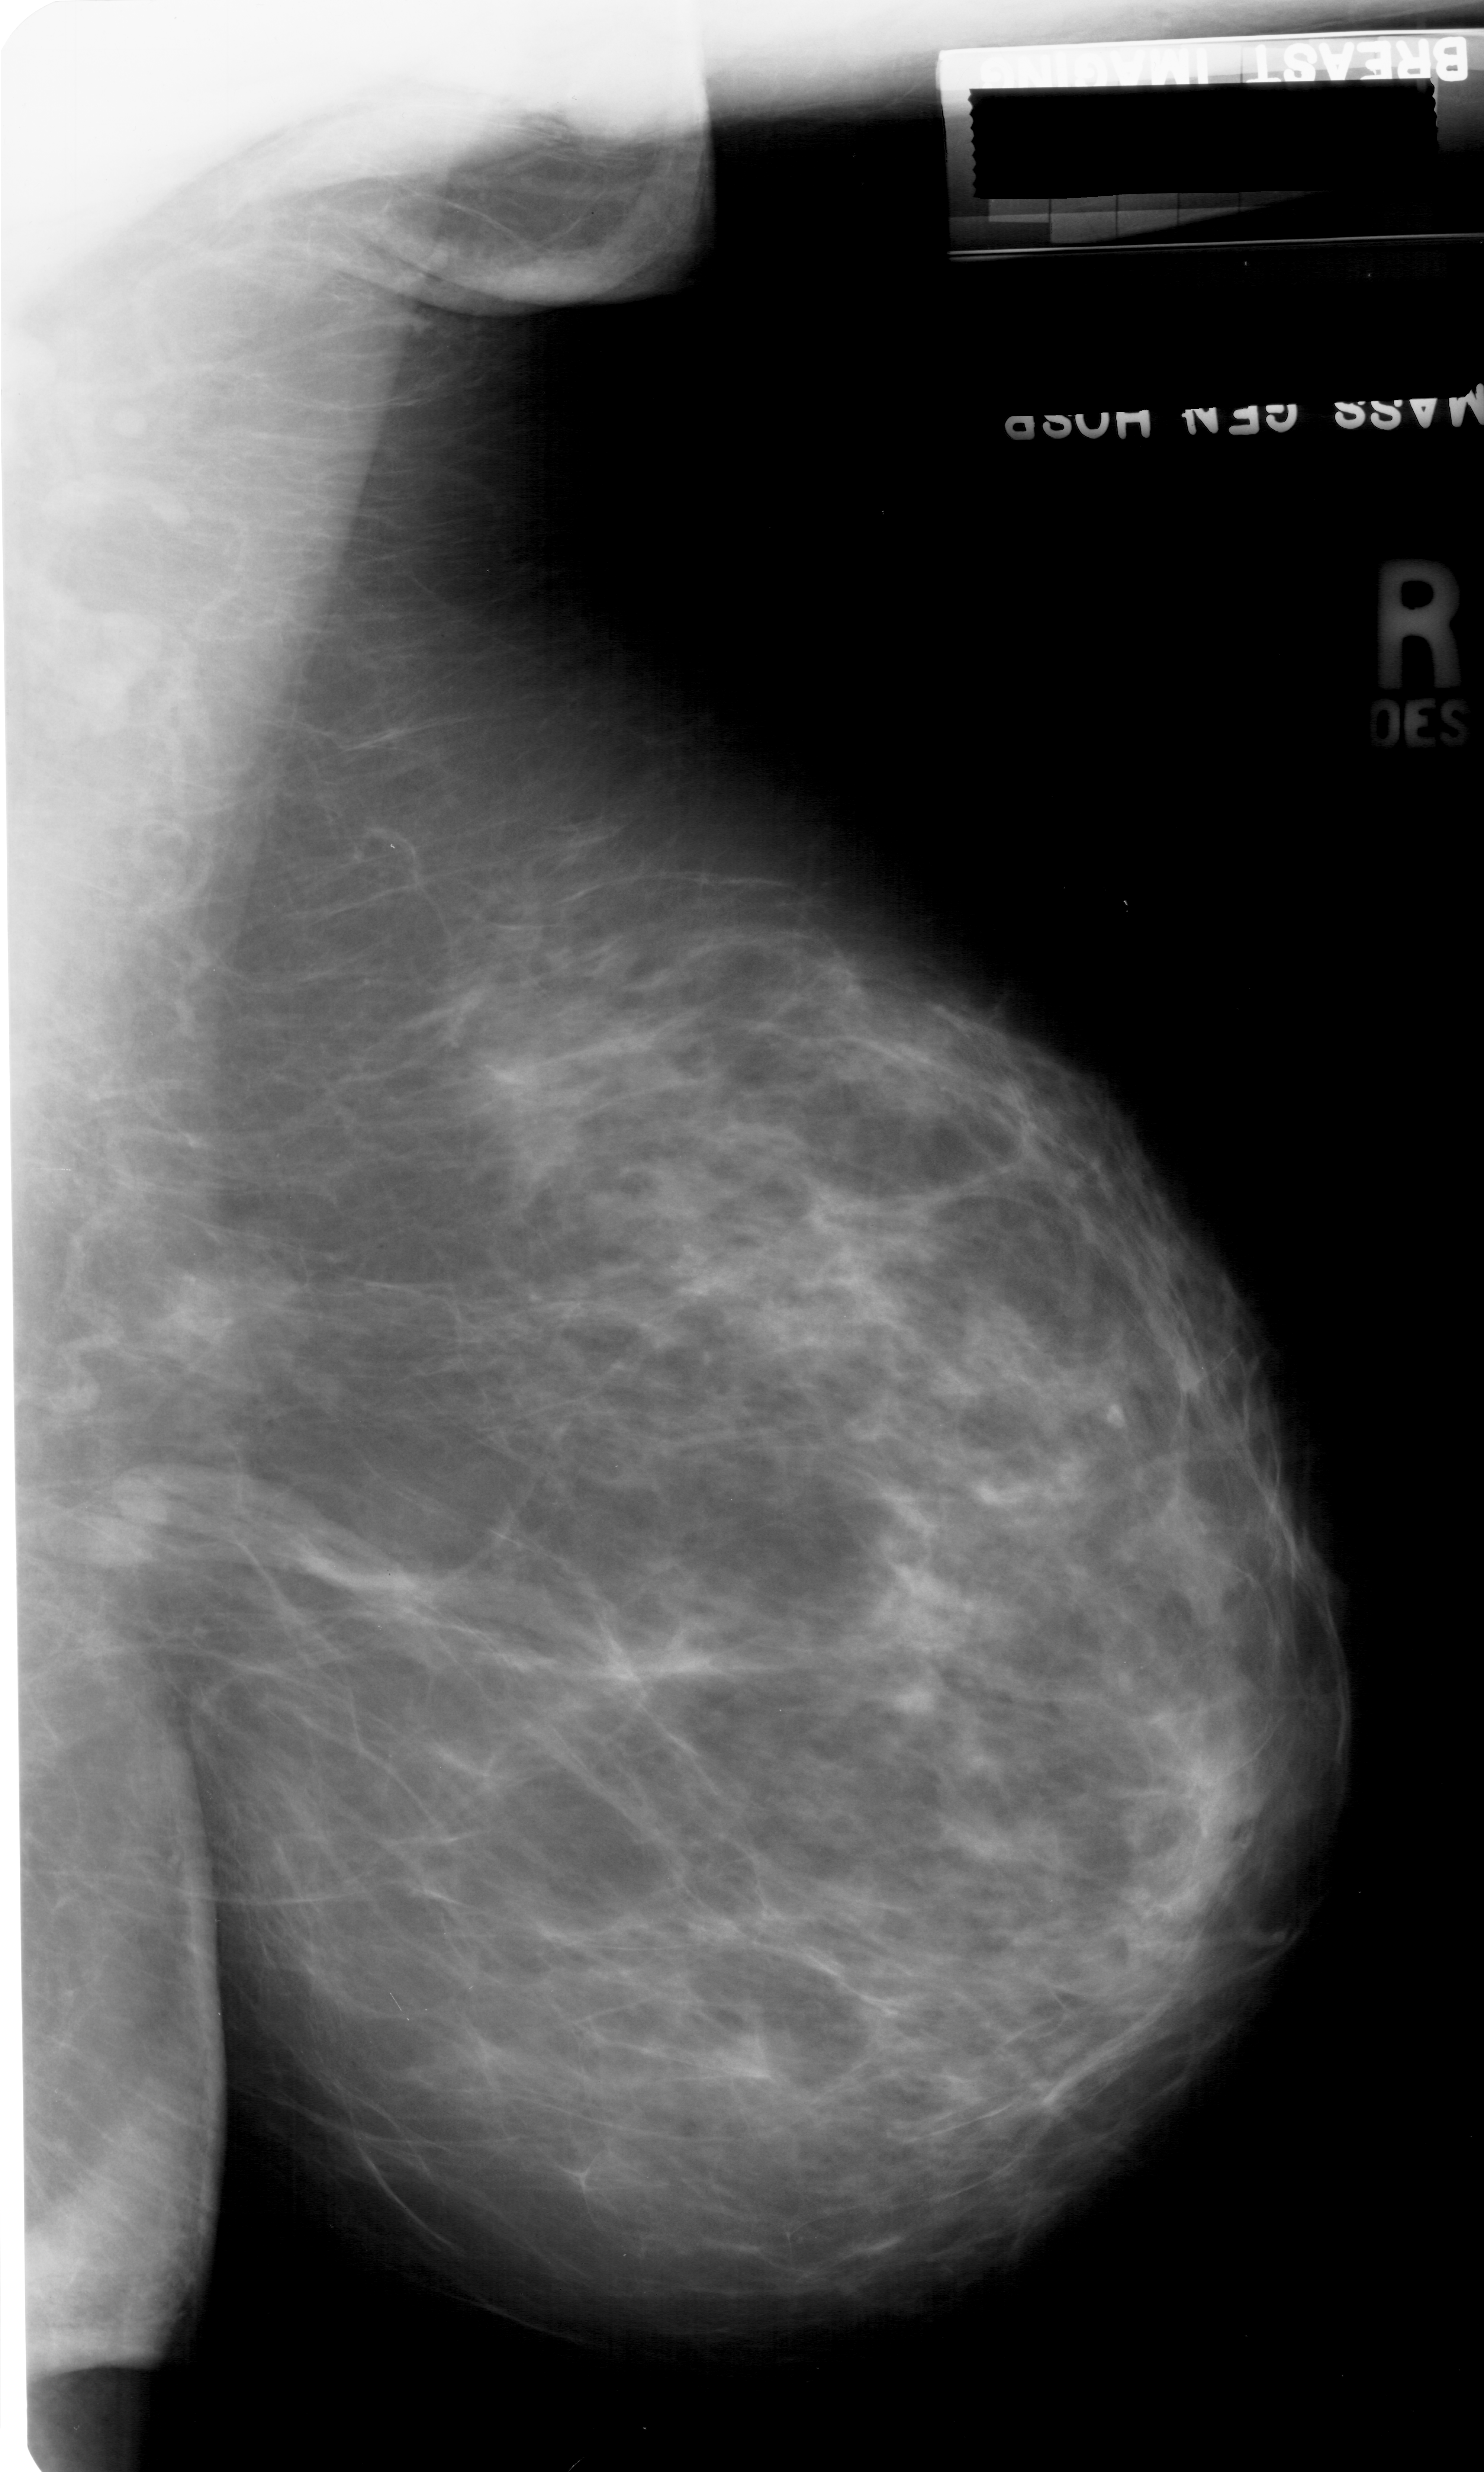
Digitized screen-film mammogram. Right breast. Mediolateral oblique (MLO) view. Breast composition: heterogeneously dense (BI-RADS density category 3 of 4). 1484 × 2472 image matrix.
Marked abnormalities (boxes around the expert regions of interest):
- mass, shape irregular, margins ill defined; BI-RADS assessment category 4; subtlety rating 2 on a 1 (subtle) to 5 (obvious) scale; pathology result (as recorded, not read from the image): benign: bounding box [x1, y1, x2, y2] px = [140, 1252, 263, 1377]